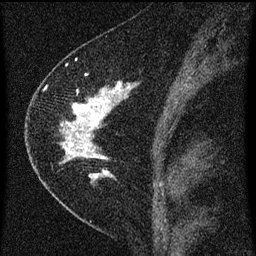
Breast MRI (dynamic contrast-enhanced), one sagittal slice; position 35 of 60 along the scan axis; dynamic contrast-enhanced series, image 2 of 3 at this slice position (ordered by acquisition); 1.5 T; TE 4.2 ms, TR 8 ms; 256 × 256 image matrix, field of view 180 × 180 mm. Female patient, age 47 years.
Structures marked on this image (semi-automatically segmented with operator editing):
- analysis volume of interest (the breast-tissue region the enhancement analysis was run in; not a lesion): box from (x=38, y=76) to (x=136, y=193) px
- tumour enhancement mask (voxels above the 70 % enhancement threshold inside the analysis volume of interest): (x=61, y=84)–(x=130, y=179)